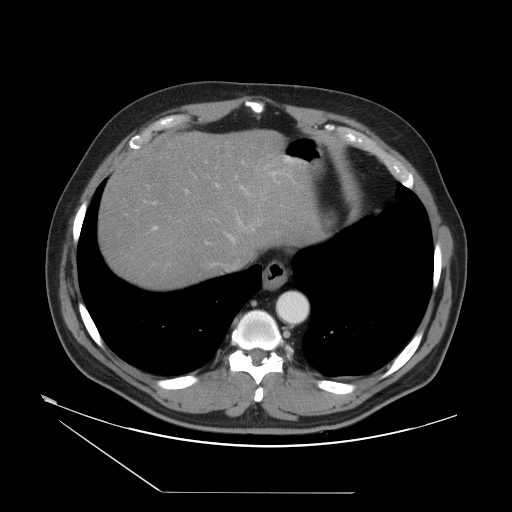
Contrast-enhanced abdominal CT, one axial slice; position 44 of 55 along the scan axis; reconstruction kernel STANDARD; intravenous contrast given; soft-tissue window (W 400 / L 40 HU); 512 × 512 image matrix, field of view 454 × 454 mm. Male patient, age 59 years. Case-level facts recorded for this patient, not image findings: diagnosis: colorectal cancer liver metastases, imaged before liver resection; multiple liver metastases: yes; largest metastasis: 0.3 cm; disease in both lobes: yes.
Outlined on this slice (expert manual segmentation):
- hepatic veins: bounding box (x1, y1, x2, y2) in pixels: (153, 175, 267, 266)
- liver: (101, 133, 317, 286)
- planned liver remnant (the part of the liver to remain after resection): (101, 160, 249, 286)
- portal vein (with intrahepatic branches): (144, 161, 295, 266)
- liver metastasis: (221, 148, 228, 156)